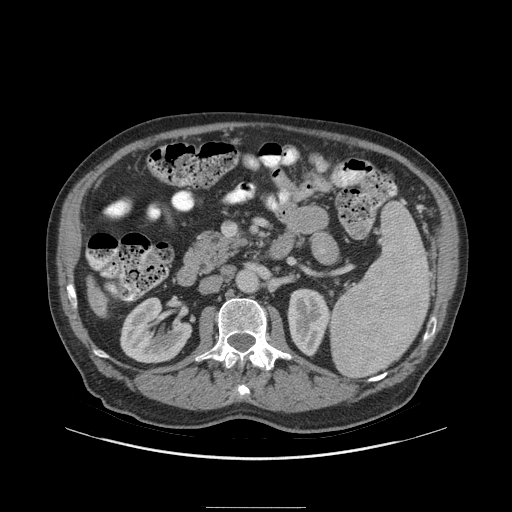
Contrast-enhanced abdominal CT (liver protocol), one axial slice. Position 27 of 105 along the scan axis. Reconstruction kernel STANDARD. 140 kVp. Soft-tissue window (W 400 / L 40 HU). 512 × 512 image matrix, field of view 440 × 440 mm. Case-level facts recorded for this patient, not image findings: diagnosis: hepatocellular carcinoma (patient treated with transarterial chemoembolisation; whether this scan precedes or follows treatment is not stated here); TNM stage (as recorded): Stage-I; Child-Pugh class: A; tumour nodularity: uninodular.
Outlined on this slice (semi-automatically segmented with operator editing):
- liver parenchyma outside the tumour (the mass and vessels are separate outlines, so this box may not span the whole liver): bounding box (x1, y1, x2, y2) in pixels: (86, 277, 106, 316)